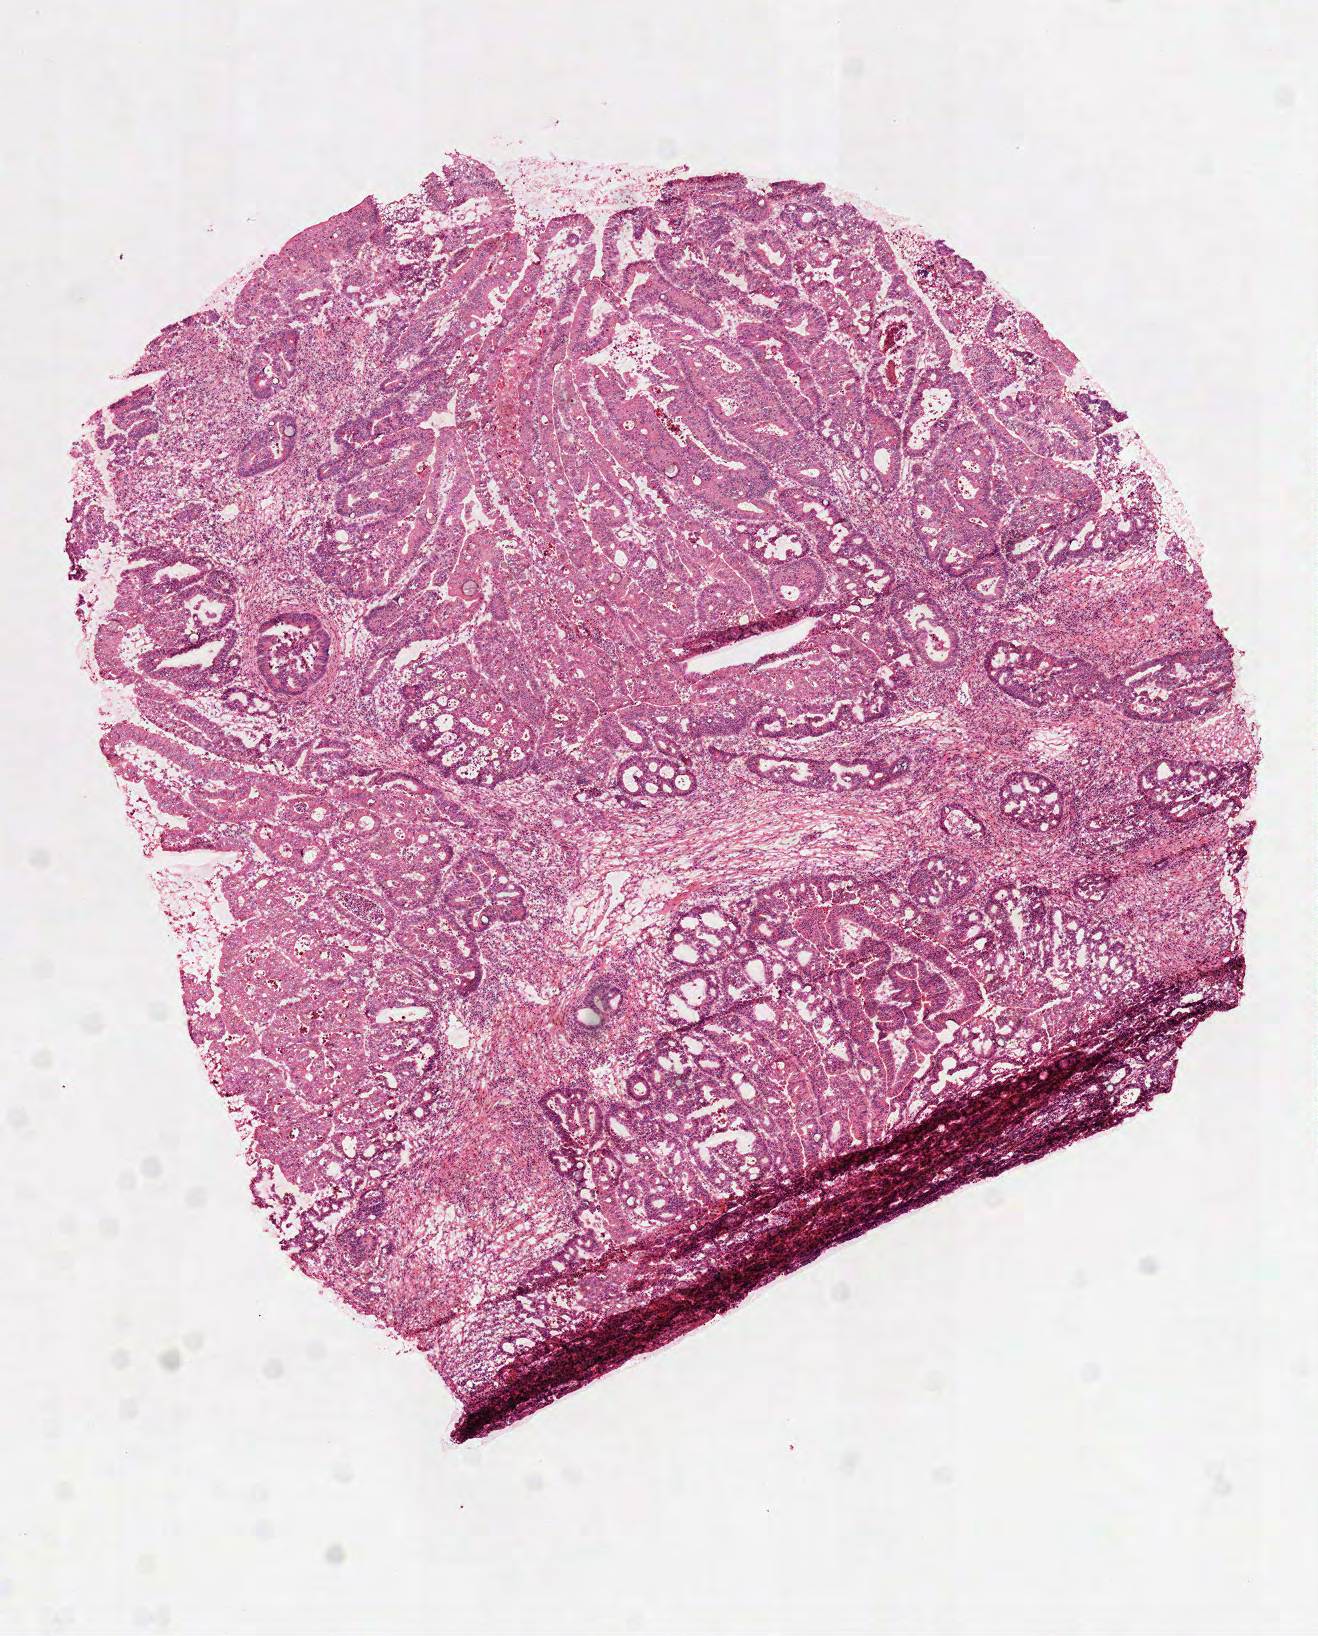
Hematoxylin and eosin (H&E) stained whole-slide image, low-resolution overview of the scanned area, about 5.3 x 6.6 mm (slide scanned at 40x), frozen section from the top of the tissue portion, sample: primary tumour, colon. Patient: female, age at initial diagnosis 80 years. Pathologist review of this section (percent, as recorded): tumour cells 98%, tumour nuclei 80%, normal cells 0%, stromal cells 0%, necrosis 2%. Inflammatory infiltration, as recorded: lymphocyte infiltration 10%, monocyte infiltration 1%, neutrophil infiltration 2%.
Lymph nodes positive (case pathology): 1 of 6 examined. AJCC pathologic stage: IIIB (7th edition). Pathologic diagnosis: Adenocarcinoma, NOS.